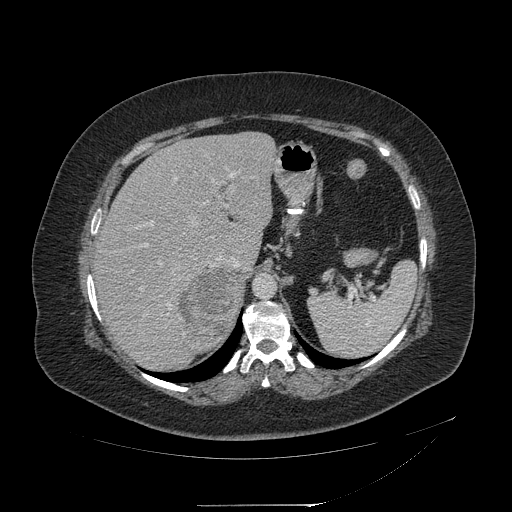
Contrast-enhanced abdominal CT, one axial slice. Slice 154 of 217 in the series (ordered by position). 120 kVp. Soft-tissue window (W 400 / L 40 HU). 512 × 512 image matrix. Patient: female, 55 years. Case-level facts recorded for this patient, not image findings: diagnosis: adrenocortical carcinoma; tumour side: right adrenal; tumour size at pathology: 11 cm; Ki-67 index: 20 %; stage (as recorded): 2.
Outlined on this slice (semi-automatic segmentation, software-assisted and operator-edited):
- mass: bounding box [x1, y1, x2, y2] px = [180, 272, 244, 350]